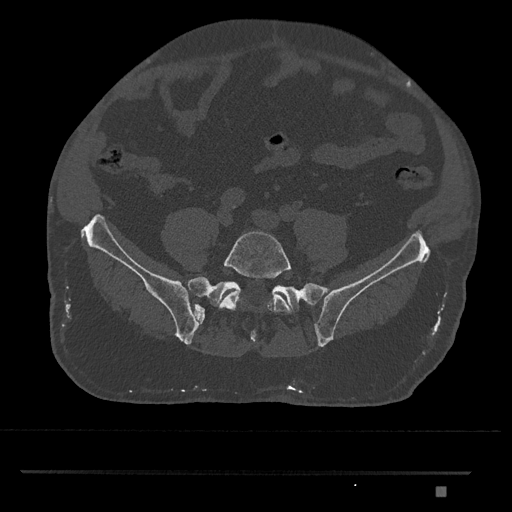
CT including the spine, one axial slice. Position 538 of 1134 along the scan axis. Reconstruction kernel Br40s/3. 120 kVp. Bone window (W 1800 / L 400 HU). 0.5 mm slice thickness. 512 × 512 image matrix, field of view 429 × 429 mm. Male patient, age 65 years. Case-level facts recorded for this patient, not image findings: primary cancer: prostate.
Annotated regions visible in this slice (semi-automatically segmented with operator editing):
- L5 vertebra: bounding box (x1, y1, x2, y2) in pixels: (219, 231, 291, 314)